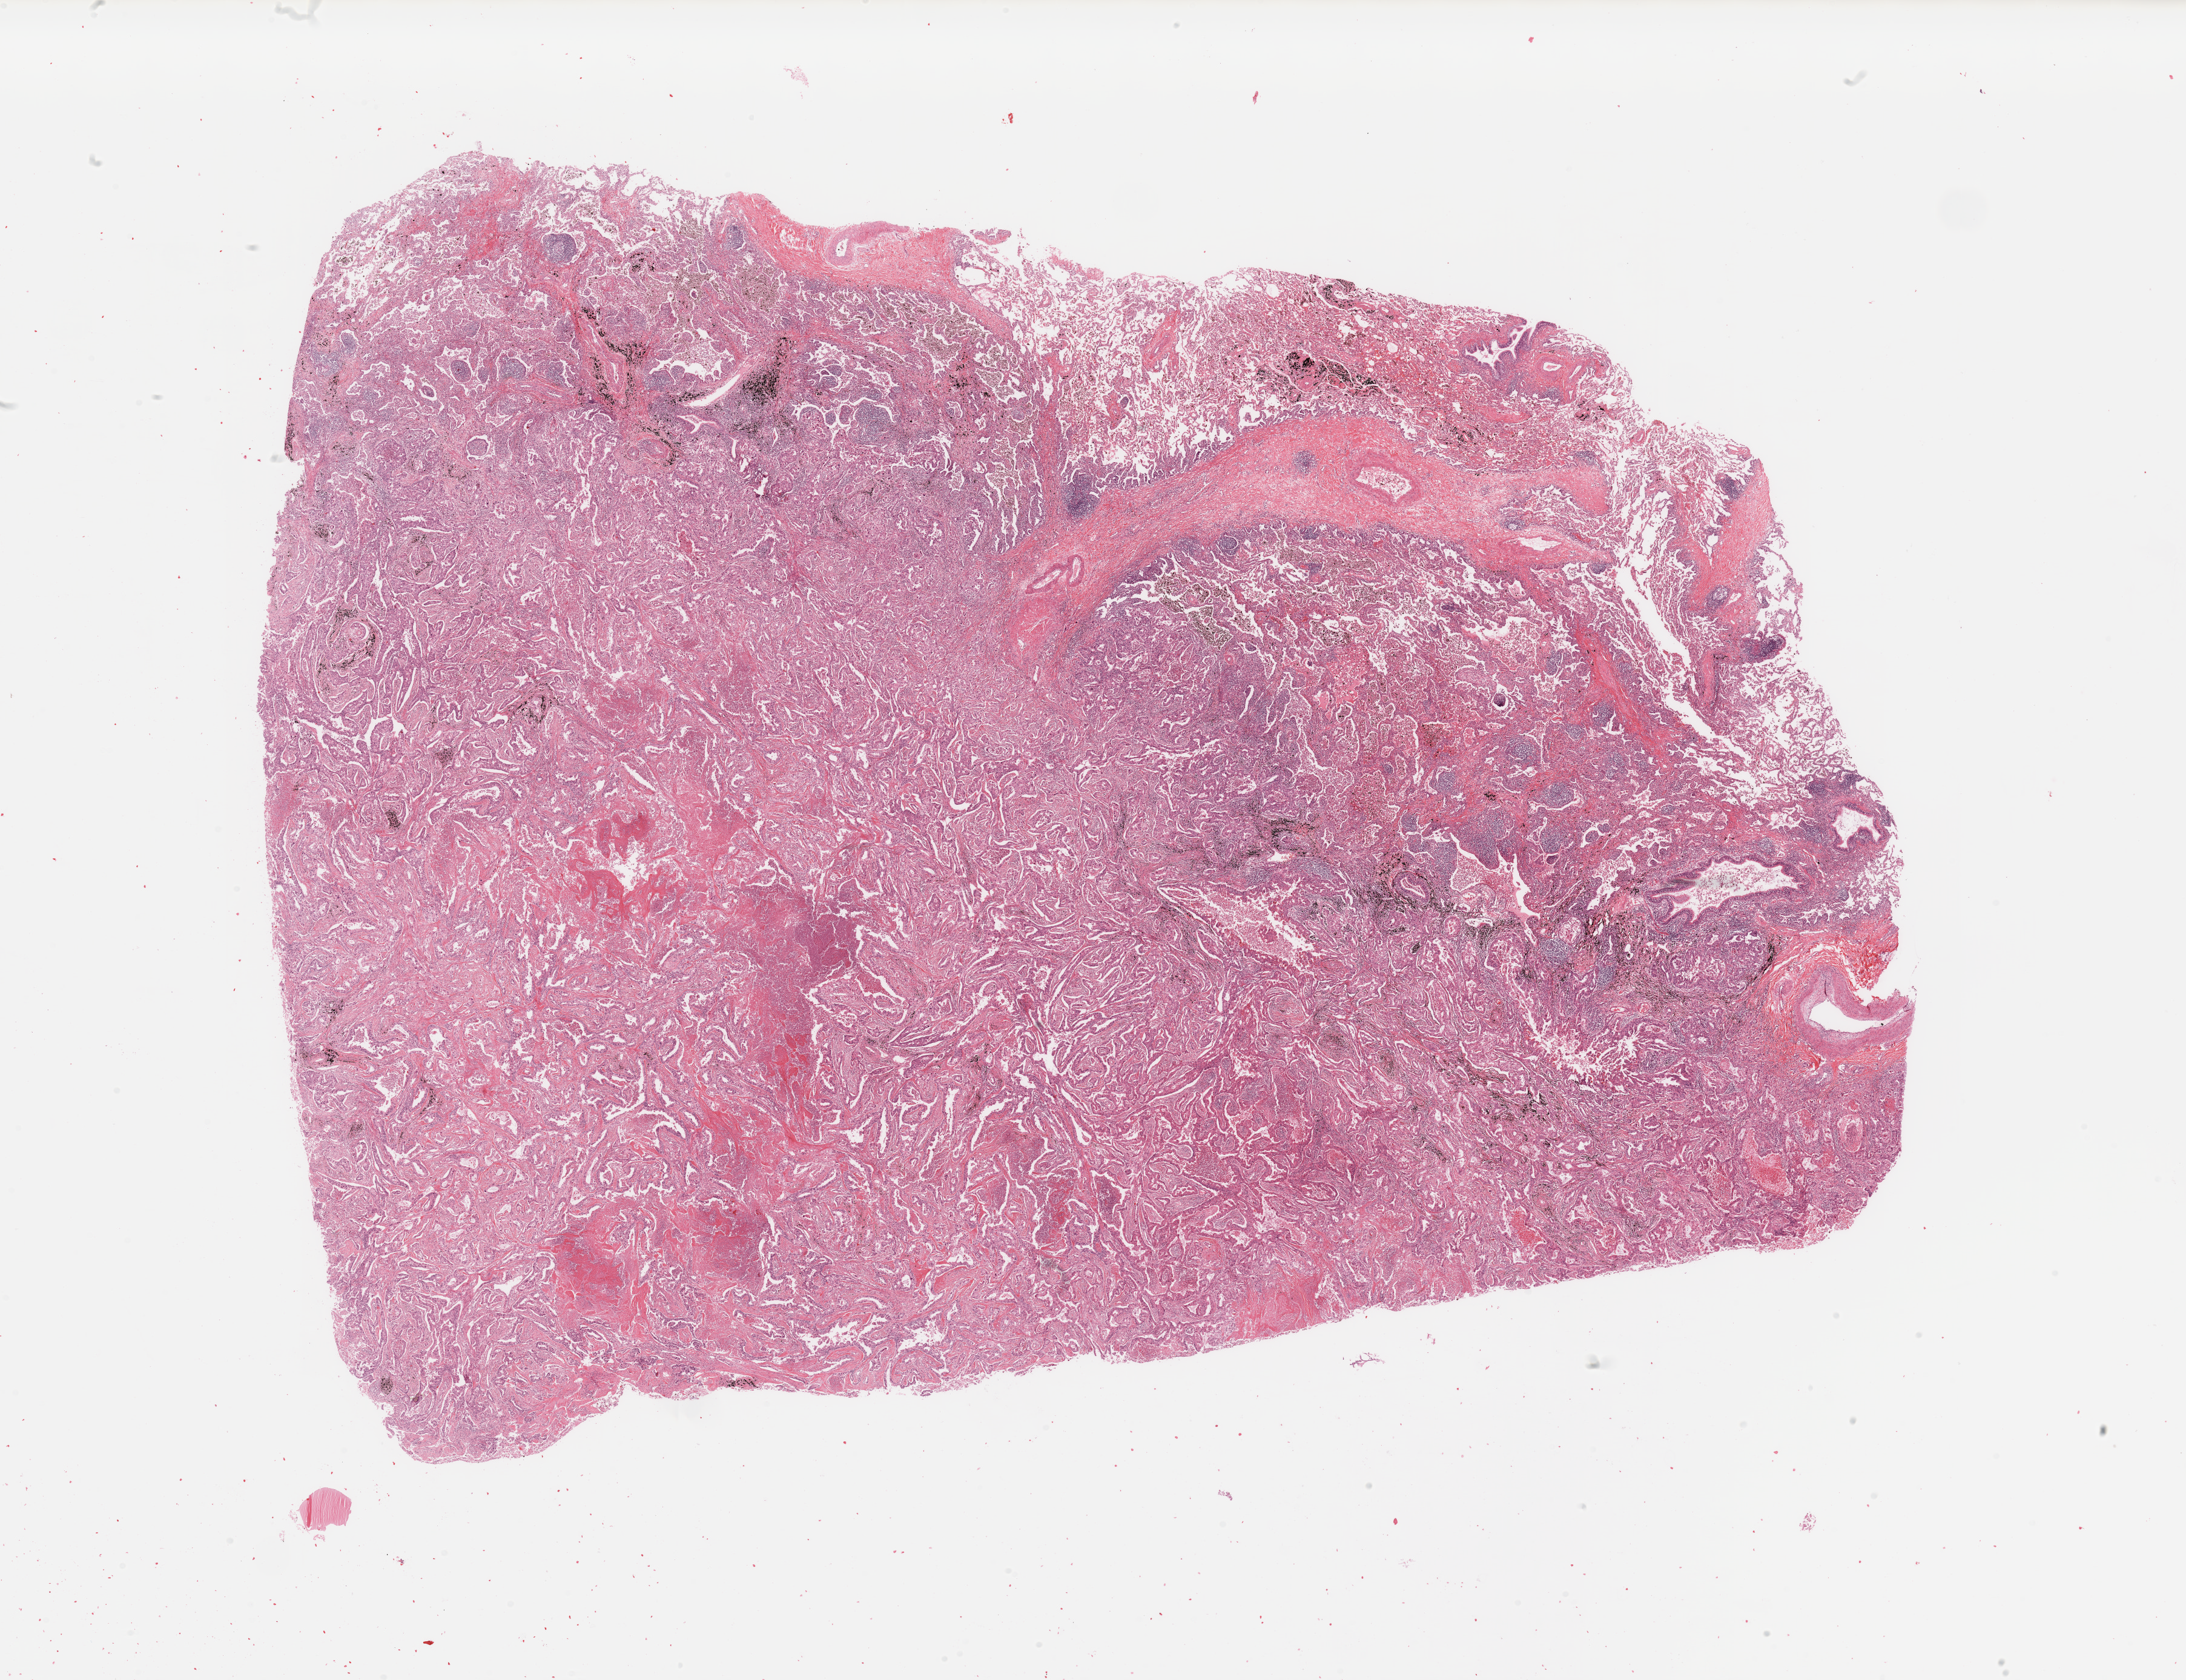
Whole-slide histology image, H&E — a low-resolution overview of the entire scanned area, about 28.5 x 21.9 mm (slide scanned at 20x), tumour tissue sample, lung. 64-year-old male patient. Histologic grade: G2 (moderately differentiated).
- histologic diagnosis: Adenocarcinoma, NOS
- AJCC pathologic stage: IIB